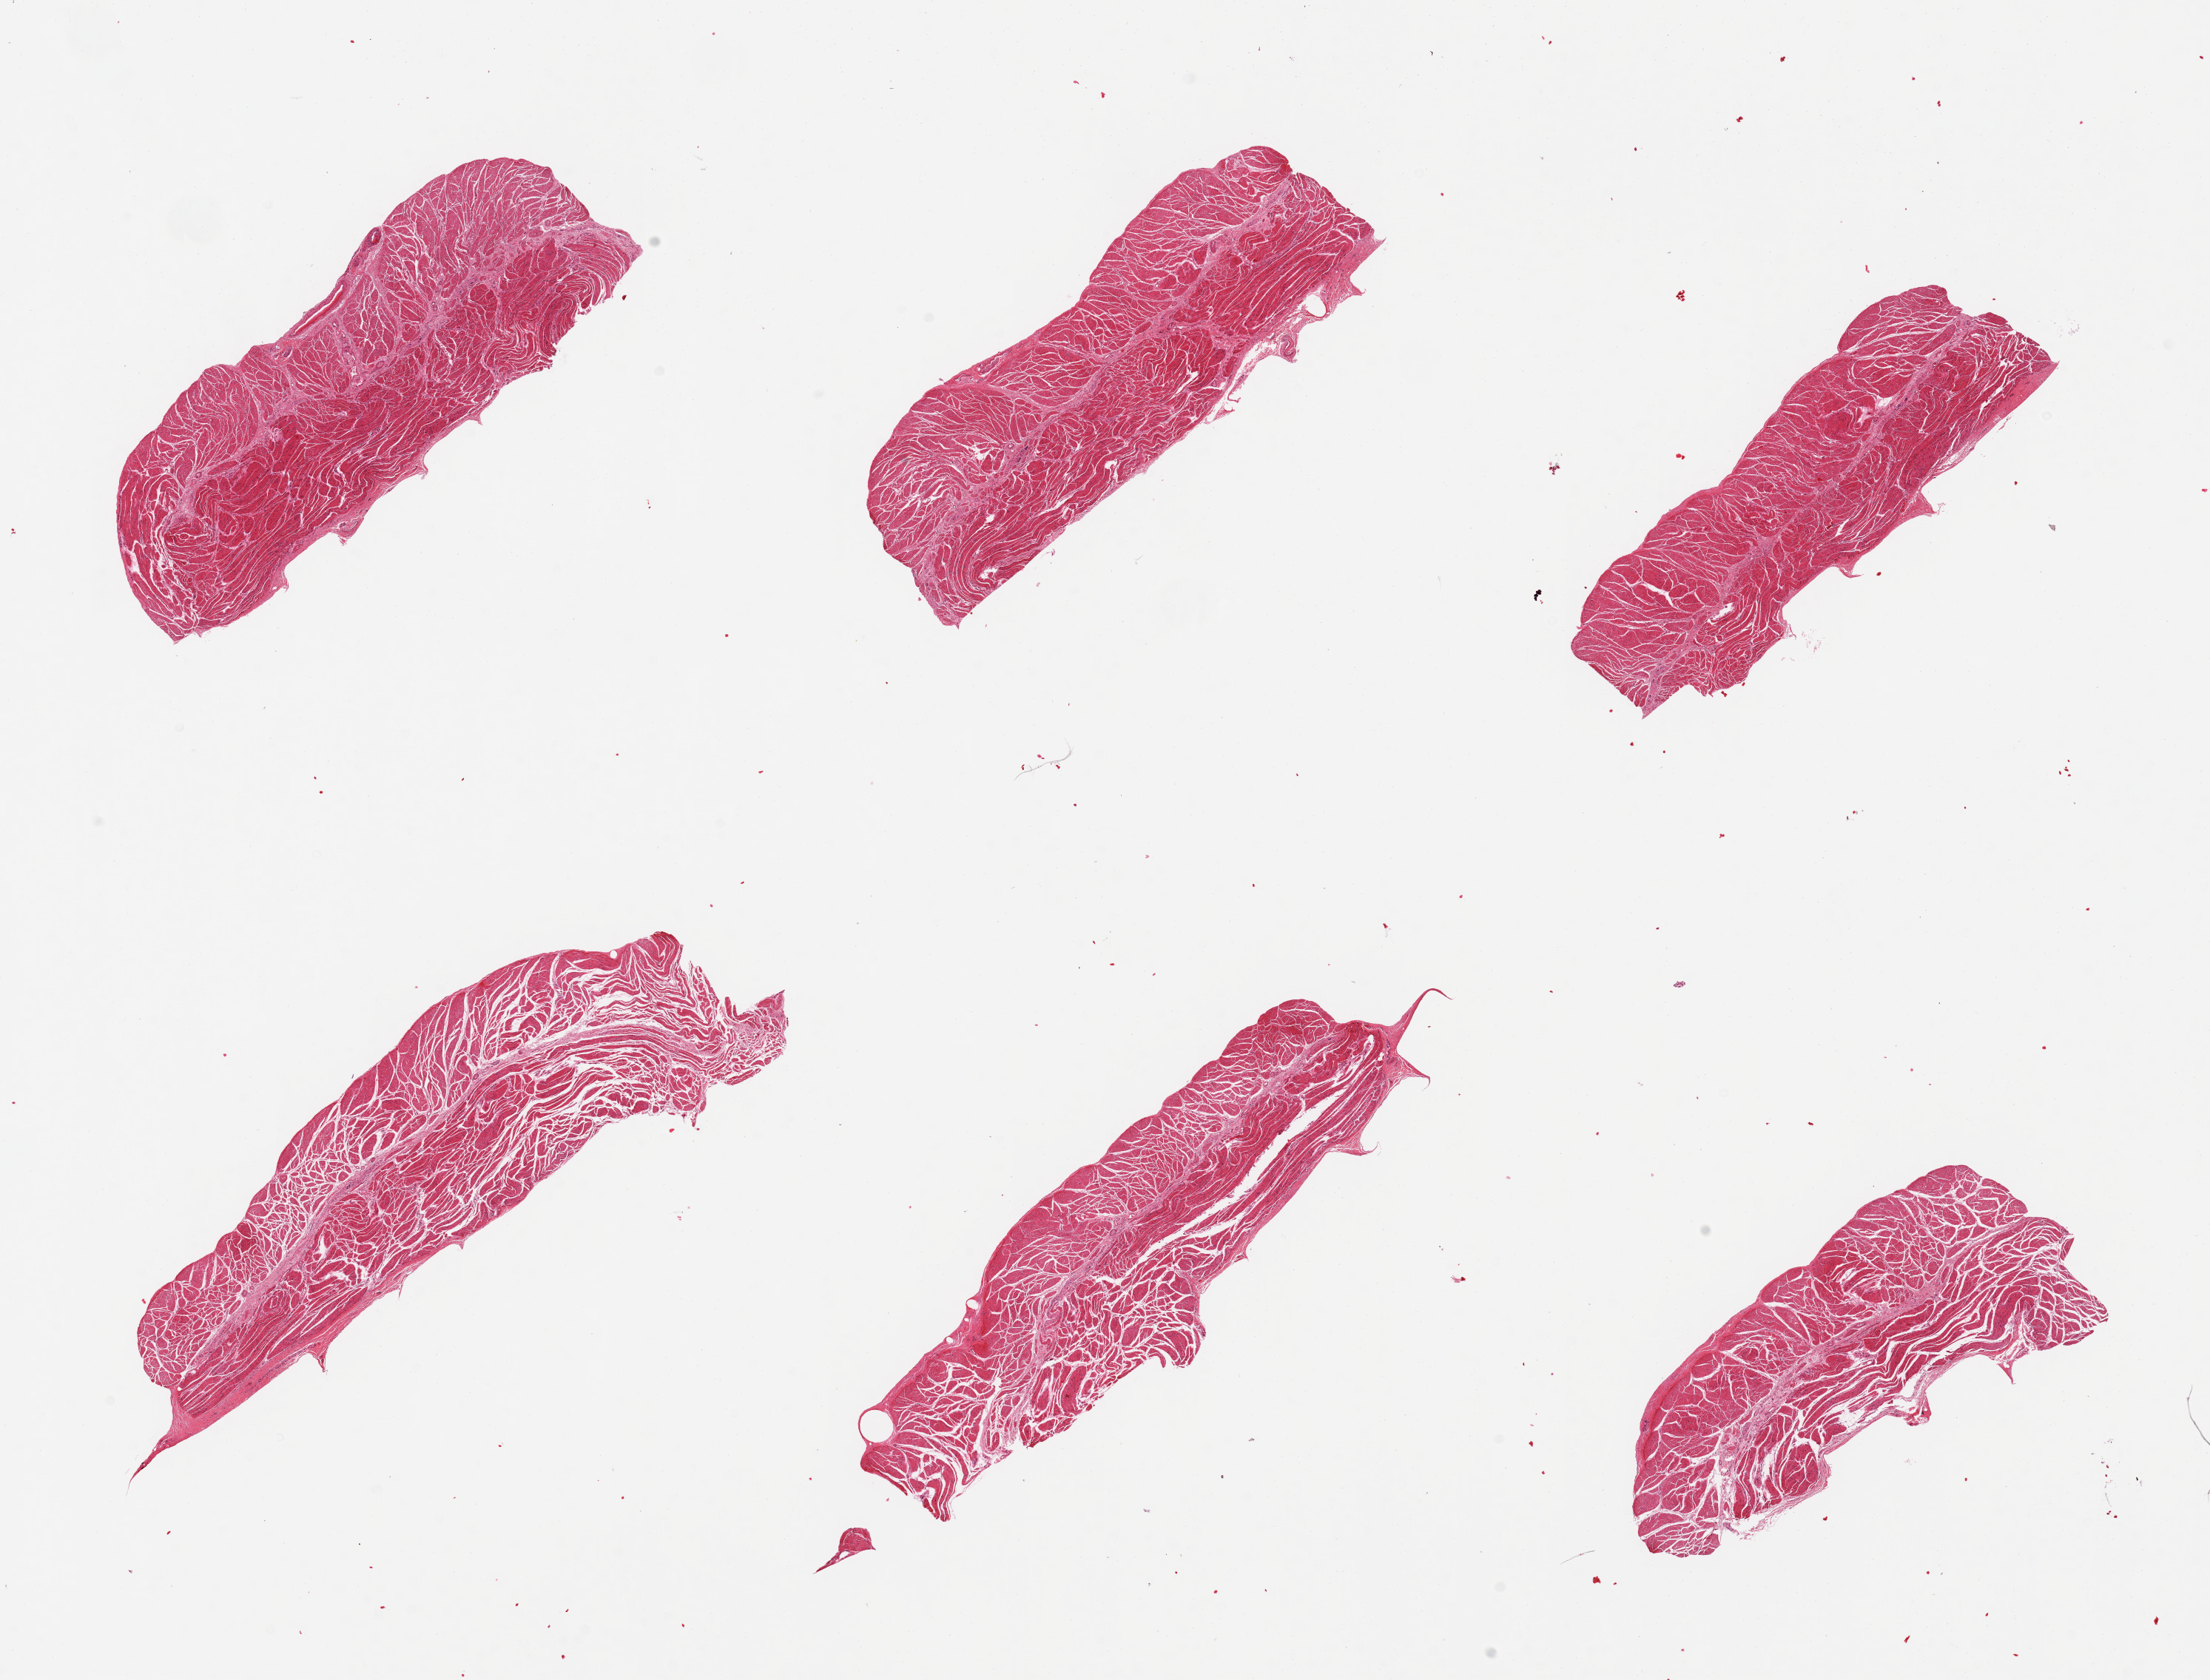
Haematoxylin and eosin whole-slide image, a low-resolution overview of the entire scanned area, about 23.6 x 18.0 mm. PAXgene-fixed, paraffin-embedded tissue. Sampled site (target tissue): gastroesophageal junction. Donor tissue sample. Donor: male.
• pathologist's review note for this sample: 6 pieces, all muscularis, good specimens